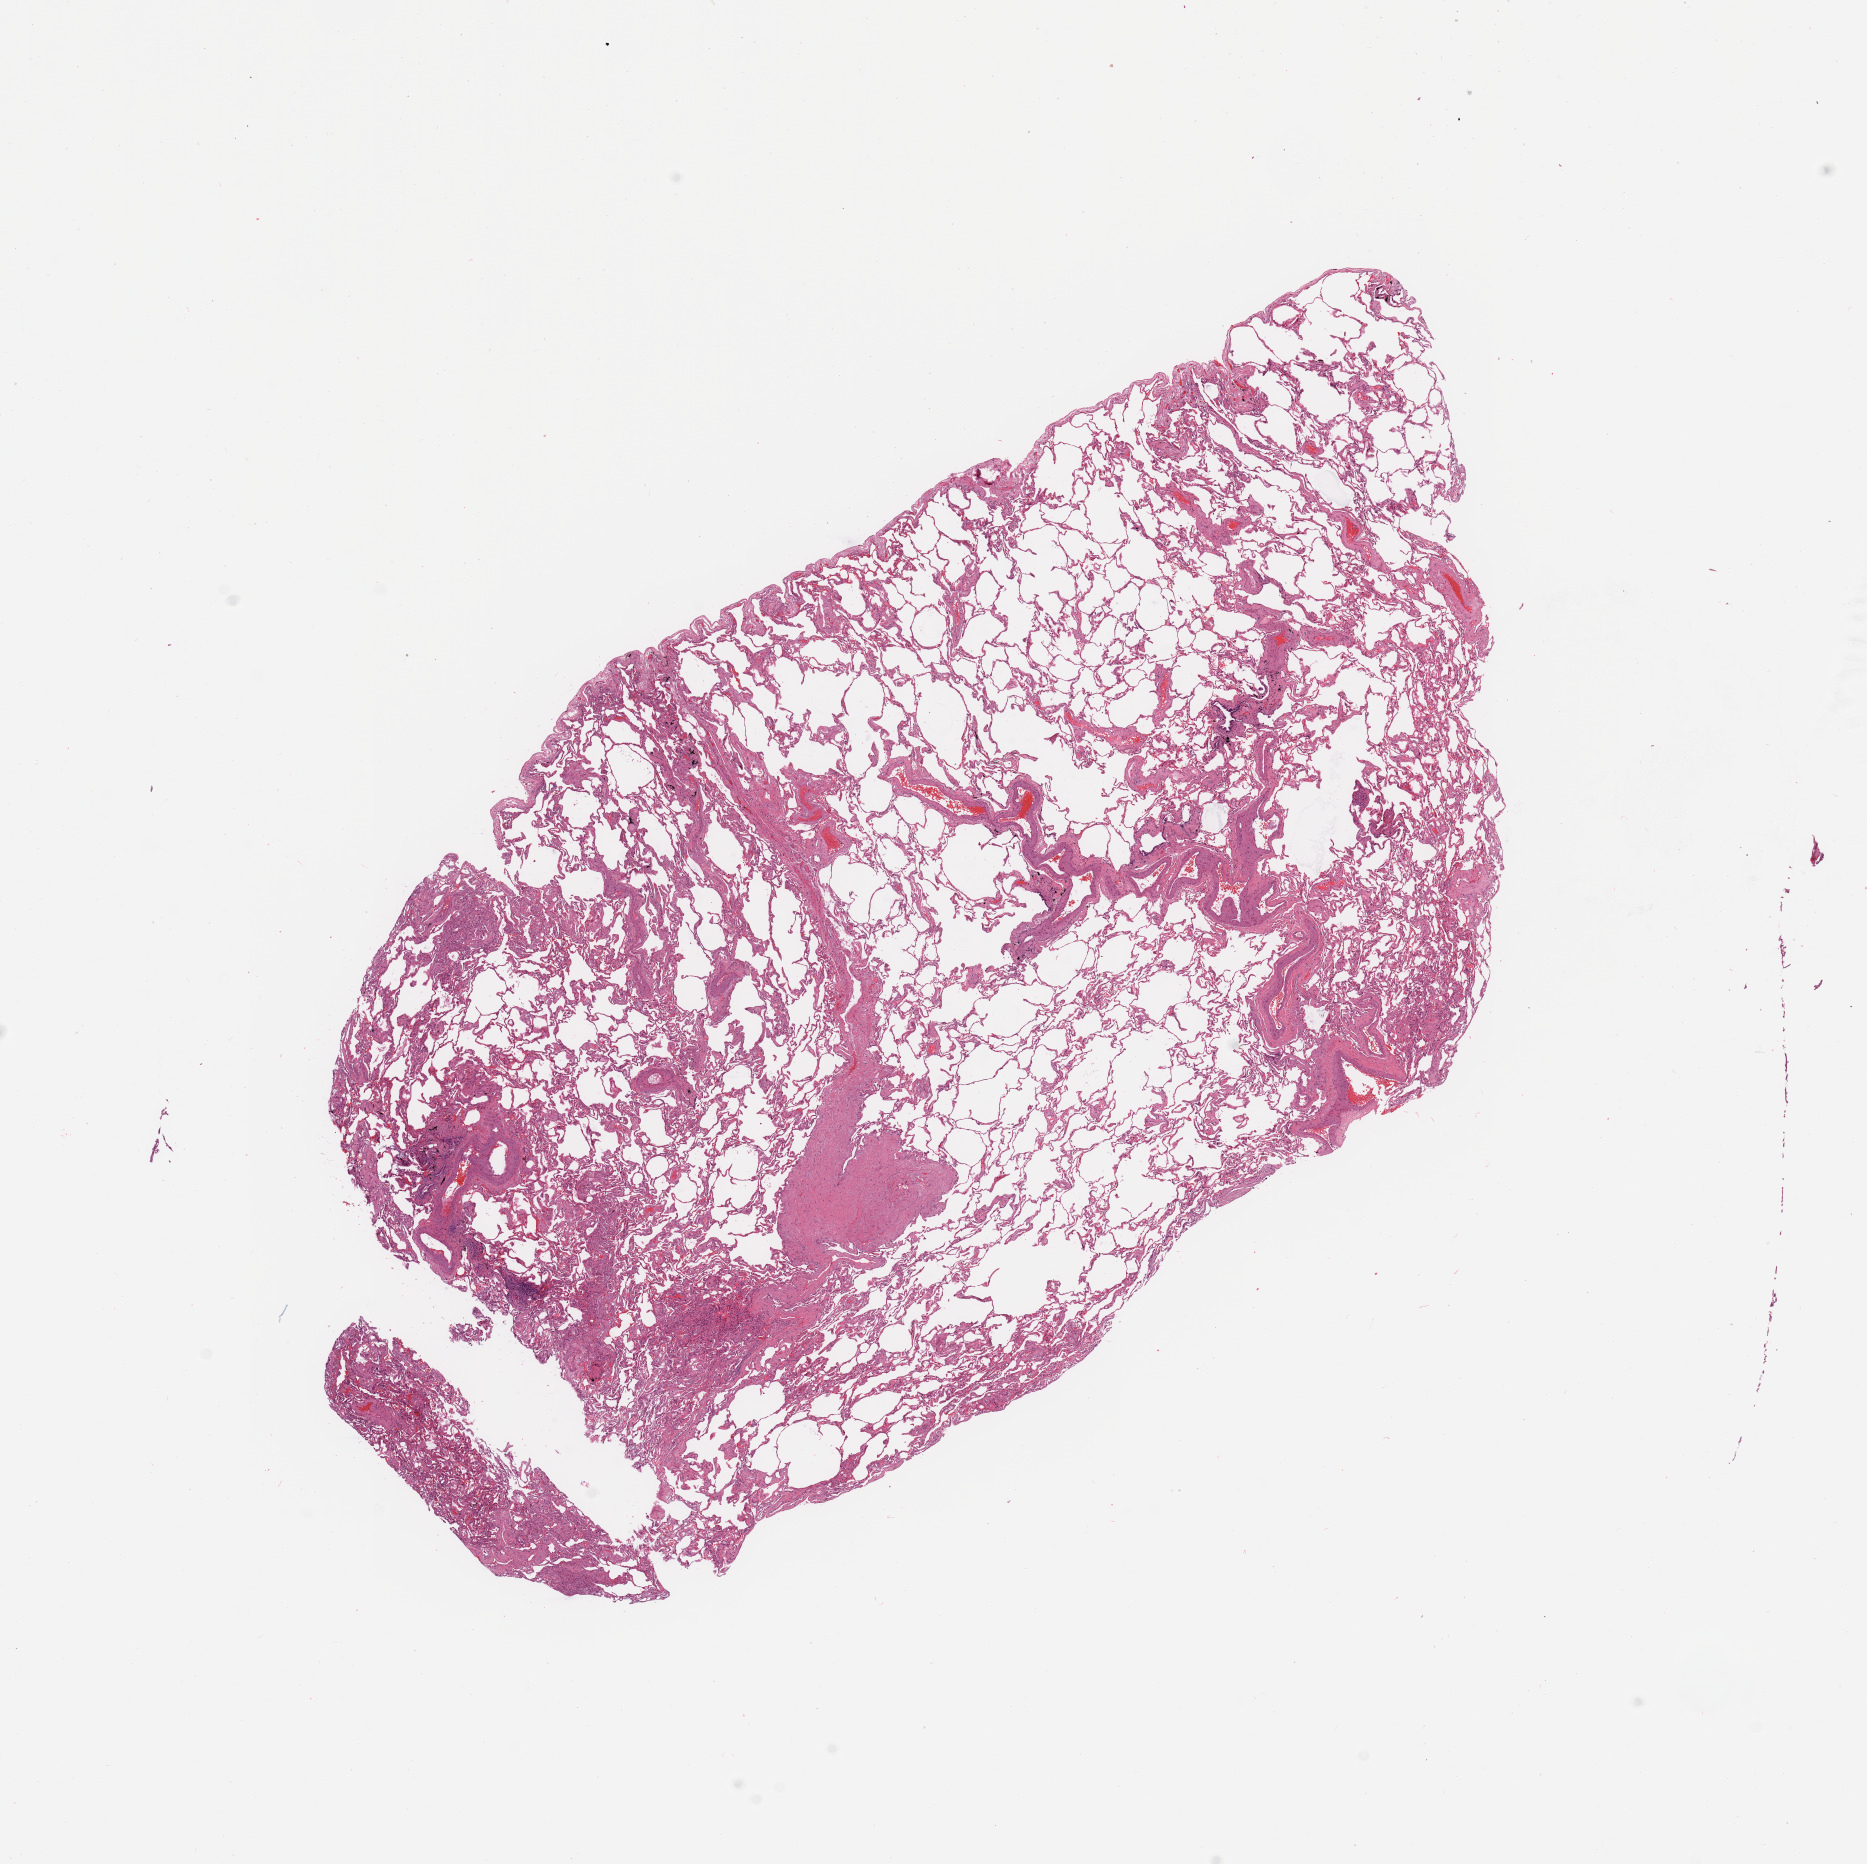
Hematoxylin and eosin (H&E) stained whole-slide image, a low-resolution overview of the entire scanned area, about 14.8 x 14.7 mm, normal (non-tumour) tissue sample, lung. Male, 77 y/o.
- this section: normal (non-tumour) tissue from the same patient
- patient diagnosis: Adenocarcinoma, NOS